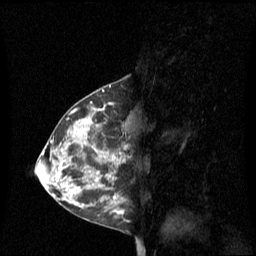
Breast MRI (dynamic contrast-enhanced), one sagittal slice. Slice 33 of 60 in the series (ordered by position). Dynamic contrast-enhanced series, image 2 of 3 at this slice position (ordered by acquisition). 1.5 T. TE 4.2 ms, TR 8.4 ms. 2.1 mm slice thickness. 256 × 256 image matrix, field of view 240 × 240 mm. Female patient, age 42 years. From the clinical record (not read from this slice): setting: breast cancer imaged before/during neoadjuvant chemotherapy; receptor status: HR-positive, HER2-negative.
Annotated regions visible in this slice (semi-automatically segmented with operator editing):
- analysis volume of interest (the breast-tissue region the enhancement analysis was run in; not a lesion): bounding box [x1, y1, x2, y2] px = [68, 102, 127, 201]
- tumour enhancement mask (voxels above the 70 % enhancement threshold inside the analysis volume of interest): [104, 154, 119, 201]